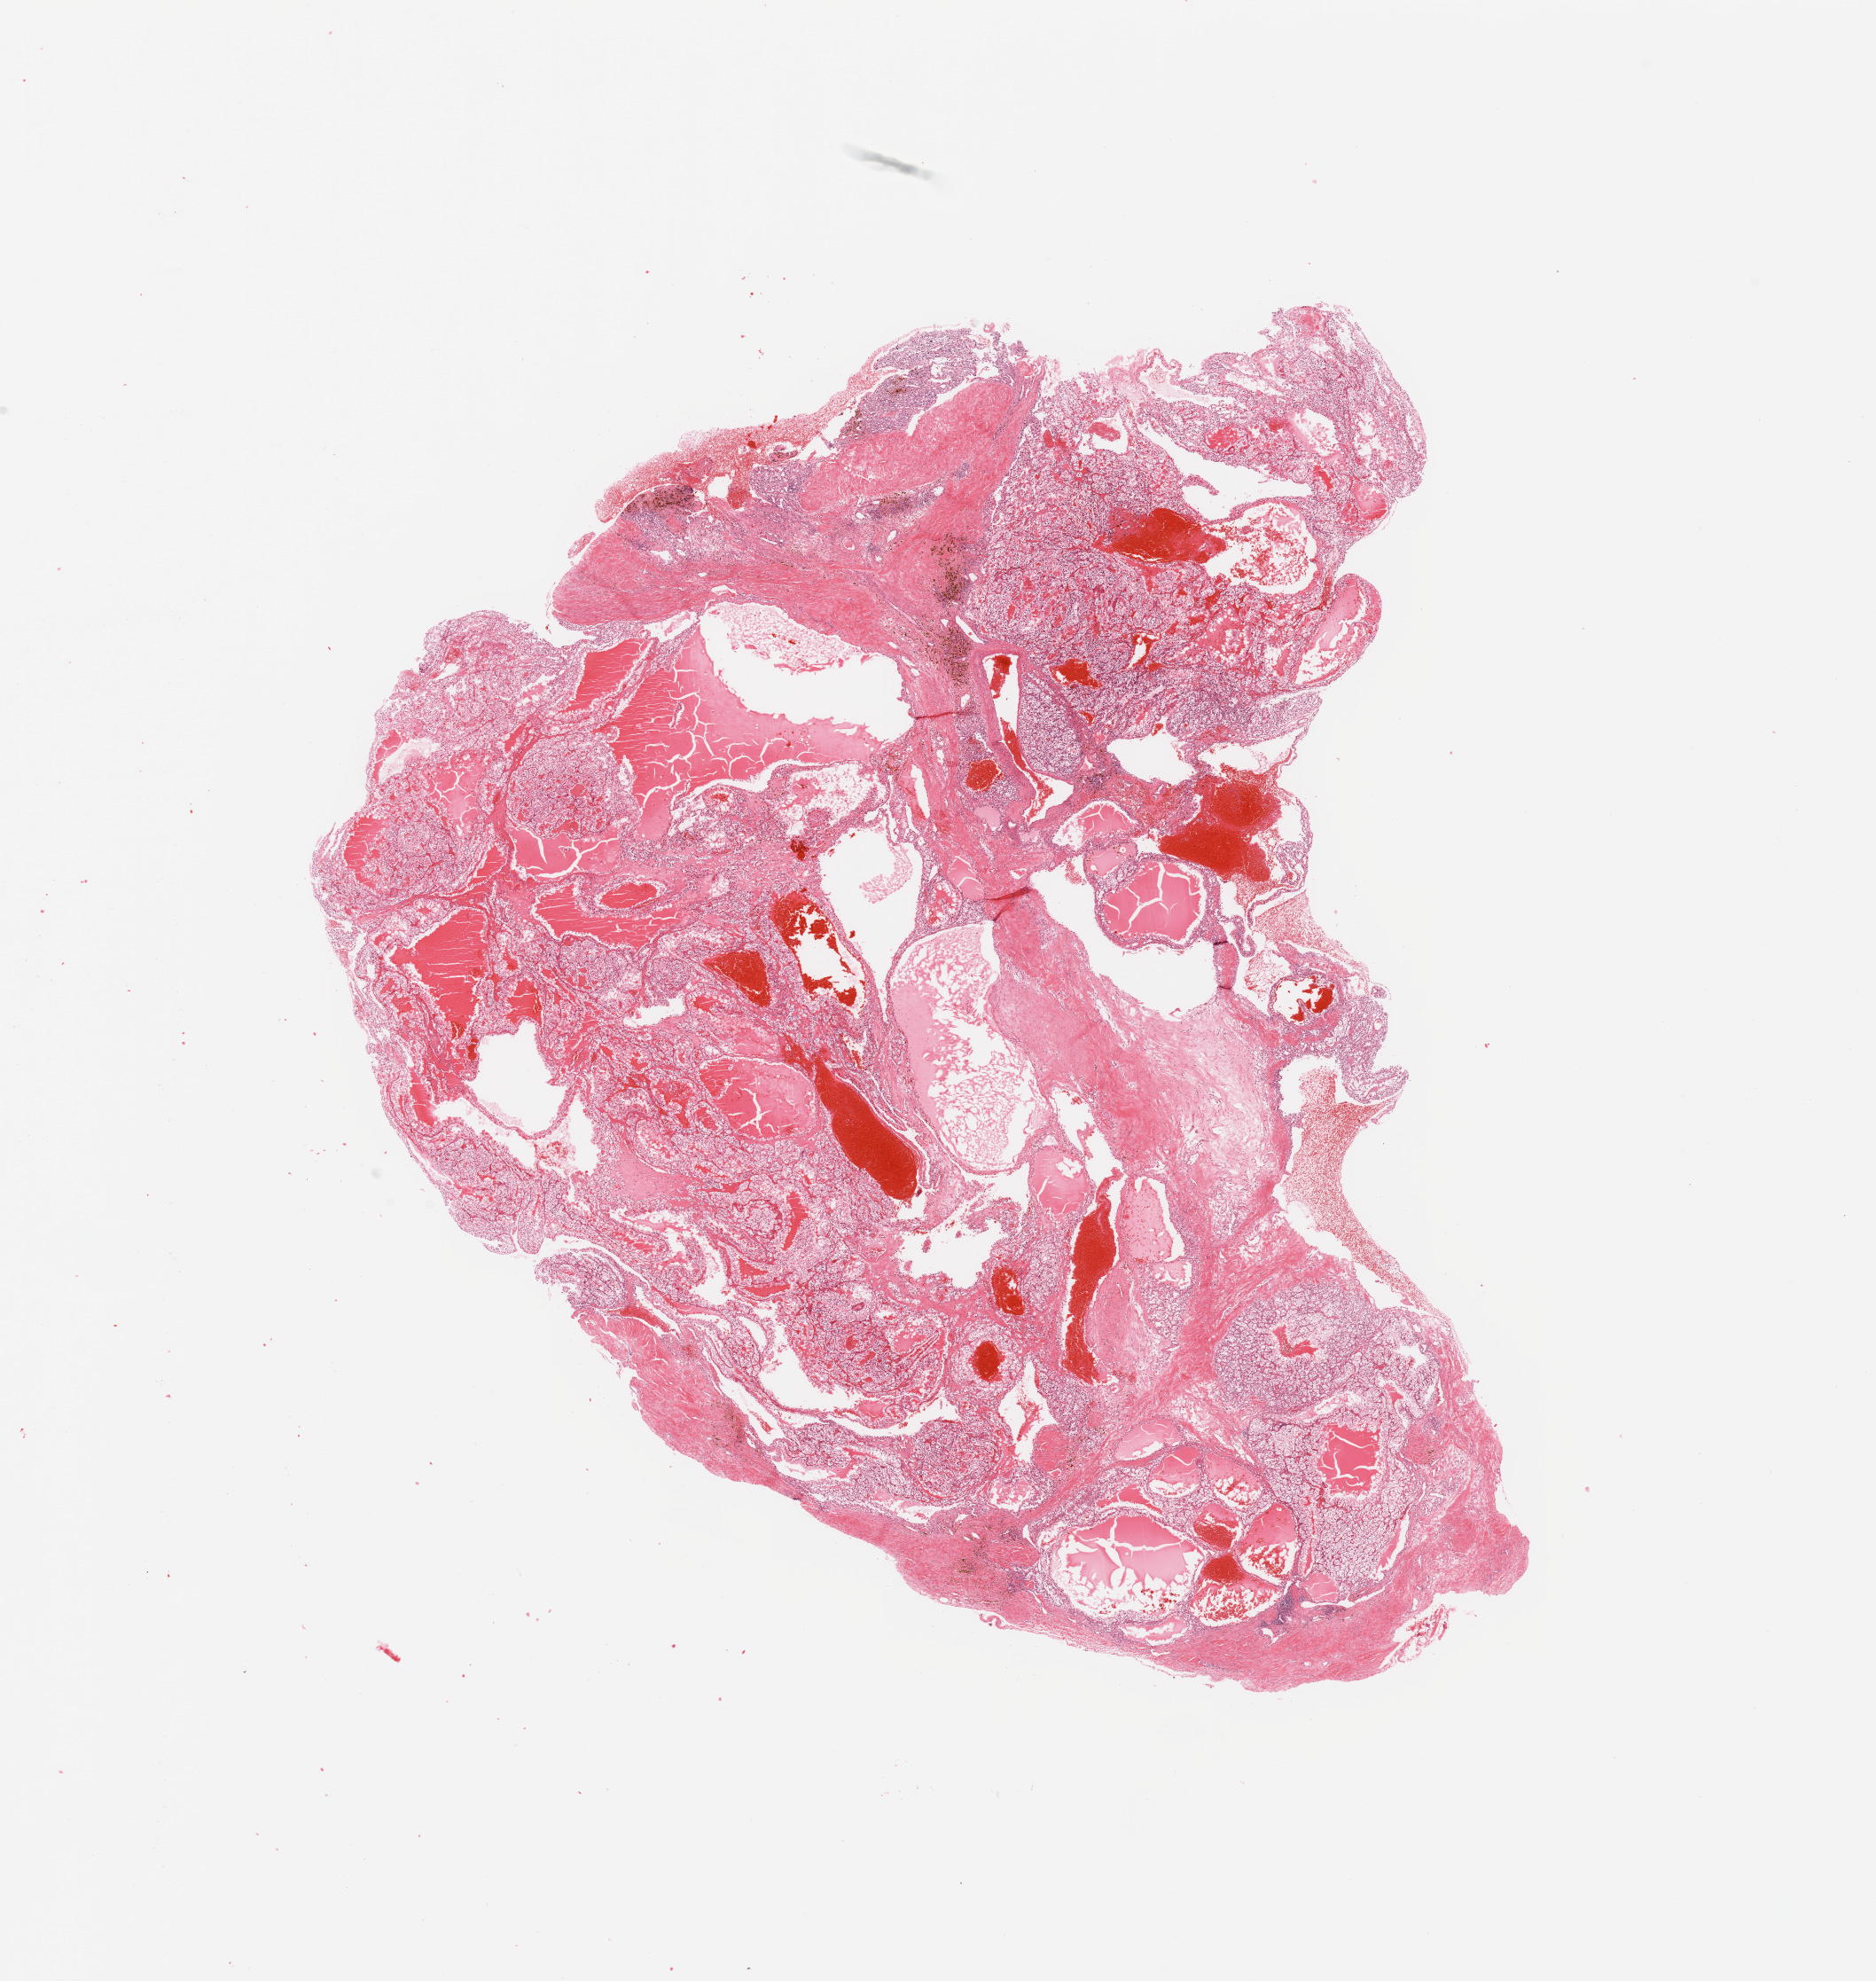
Digitized H&E-stained tissue section (whole slide), low-resolution overview of the scanned area, about 16.7 x 17.7 mm. Tumour tissue sample, sampled site: kidney. Female, 55 y/o. Histologic grade: G3 (poorly differentiated). Pathologist review of this section (percent, as recorded): tumour nuclei 85%, necrosis 15%.
Diagnosis: Renal cell carcinoma, NOS. AJCC pathologic stage: IV.